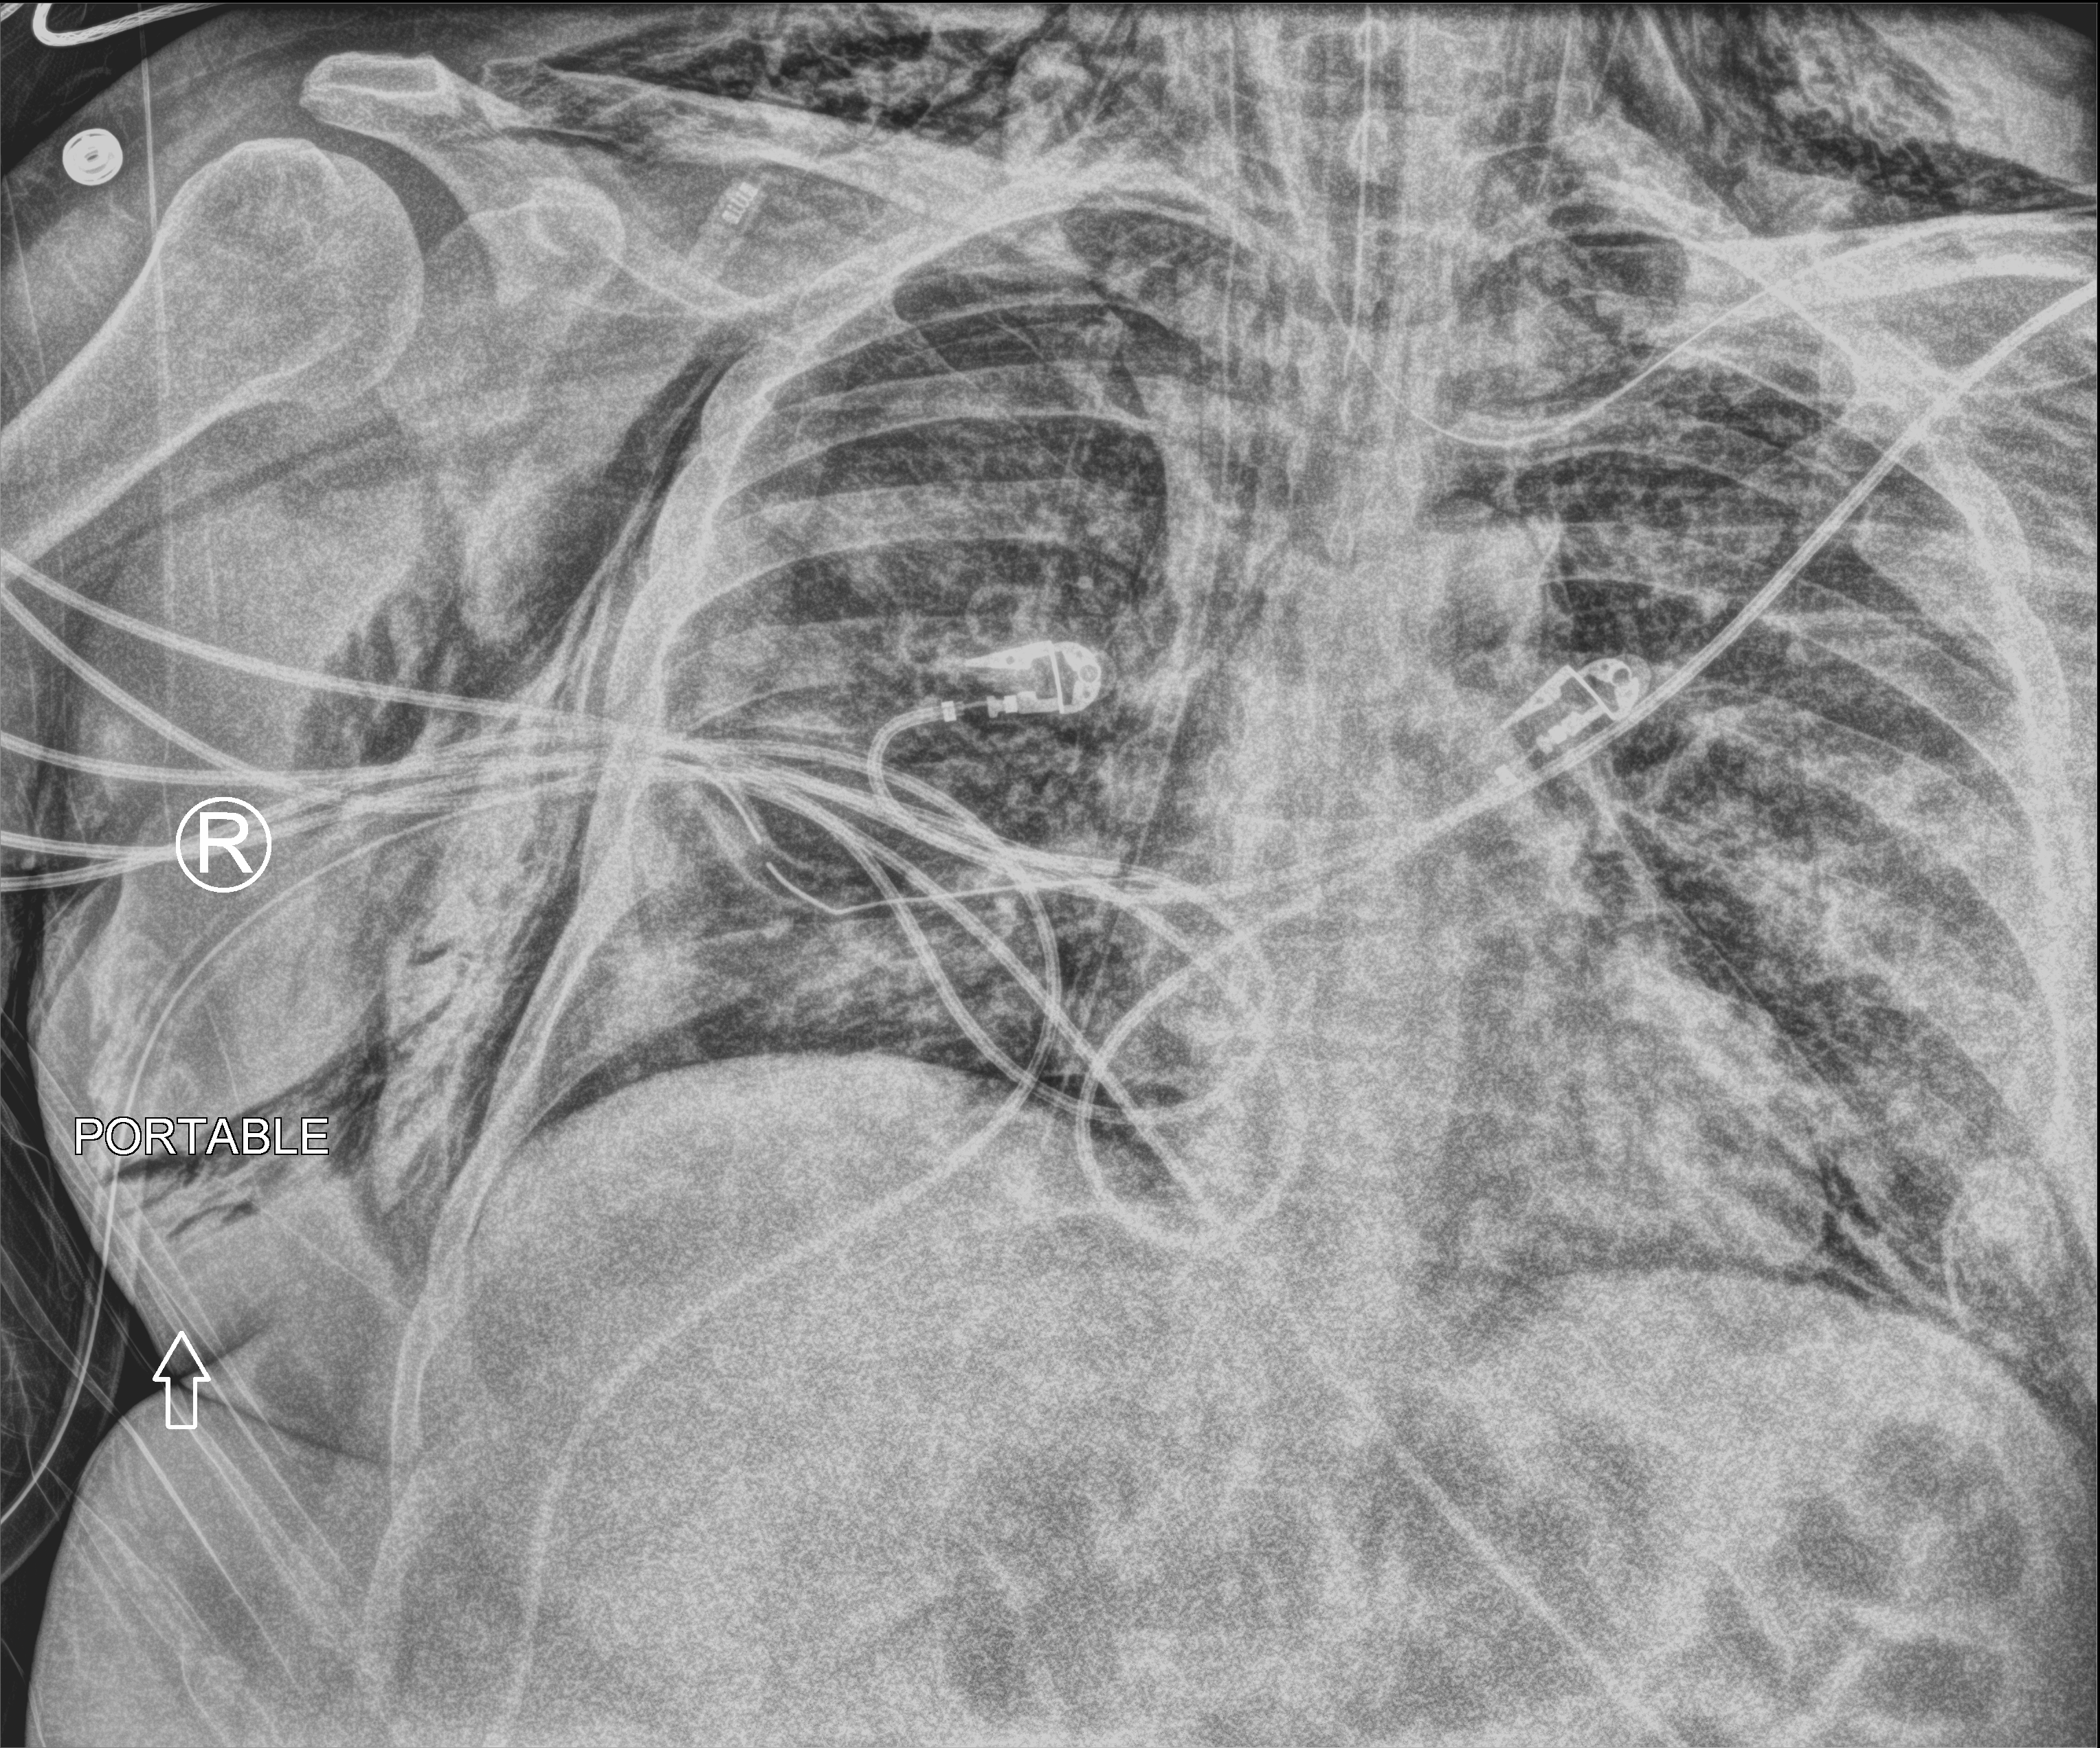
Portable chest radiograph, anteroposterior (AP) projection. Patient hospitalised with COVID-19; male, aged 18–59 years.
From the hospital-stay record, not from the radiograph (when in the stay this image was taken is not recorded):
- mechanically ventilated during this hospital stay: yes
- smoking status (admission record): never